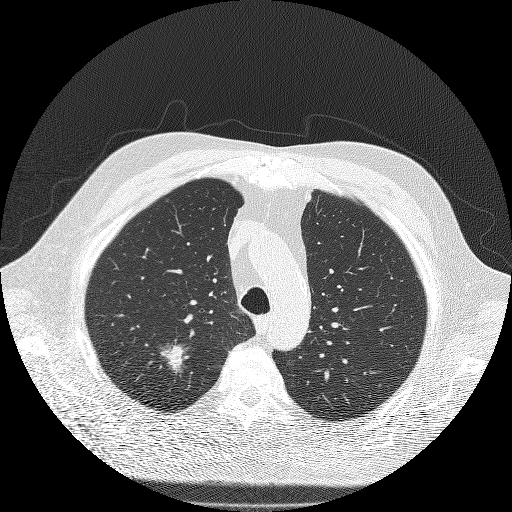
Low-dose screening chest CT, axial slice, second screening round (one year after baseline), lung window (W 1500 / L -600 HU), 2 mm slice thickness, lung (sharp) reconstruction kernel (FC51), 120 kVp, slice 34 of 180 in the series. Male, age 71 years at enrolment.
- Lesion marked by an expert reader, box from (x=139, y=327) to (x=204, y=389) px.
- The screening reader recorded 3 non-calcified nodules or masses ≥4 mm on this exam; which of them this box marks is not recorded.
- Official screen result: positive, other.
- Later outcome: lung cancer diagnosed 59 days after this screen — bronchiolo-alveolar adenocarcinoma, NOS, right upper lobe, moderately differentiated (G2), stage IIIA (AJCC 6th edition), 25 mm at pathology.